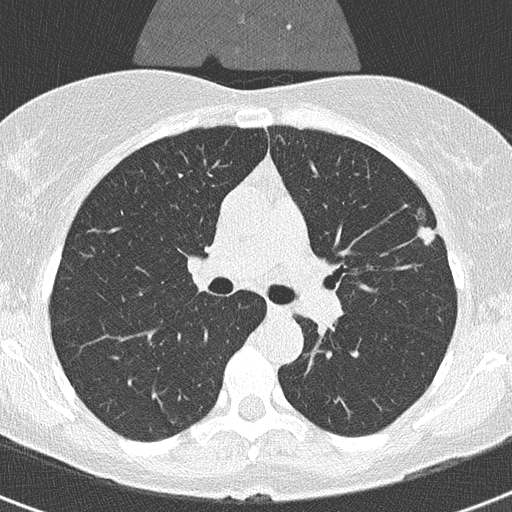
Low-dose screening chest CT, one axial slice; position 209 of 320 along the scan axis; reconstruction kernel B50f; 120 kVp; lung window (W 1500 / L -600 HU); 2 mm slice thickness; 512 × 512 image matrix, field of view 290 × 290 mm.
Outlined on this slice (manually delineated by an expert):
- lesion 1 (tumor, upper lobe of left lung): box from (x=417, y=210) to (x=435, y=245) px